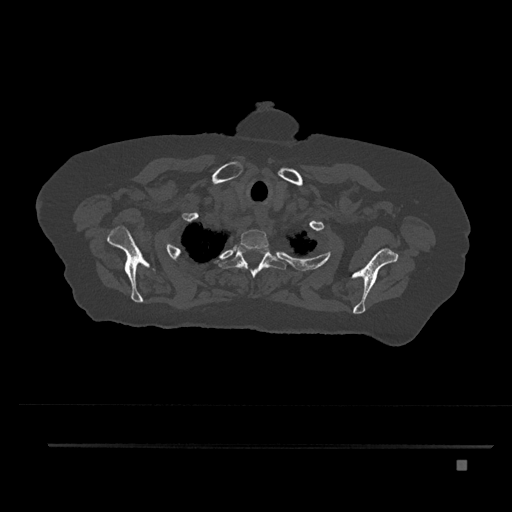
CT including the spine, one axial slice. Position 678 of 797 along the scan axis. Reconstruction kernel Br40s/3. Bone window (W 1800 / L 400 HU). 0.5 mm slice thickness. 512 × 512 image matrix. Female patient, age 76 years. From the clinical record (not read from this slice): primary cancer: lung; vertebrae with lytic lesions (as recorded): T11, L3.
Outlined on this slice (semi-automatic segmentation, software-assisted and operator-edited):
- T1 vertebra: bounding box (x1, y1, x2, y2) in pixels: (240, 229, 269, 250)
- T2 vertebra: (219, 245, 287, 277)